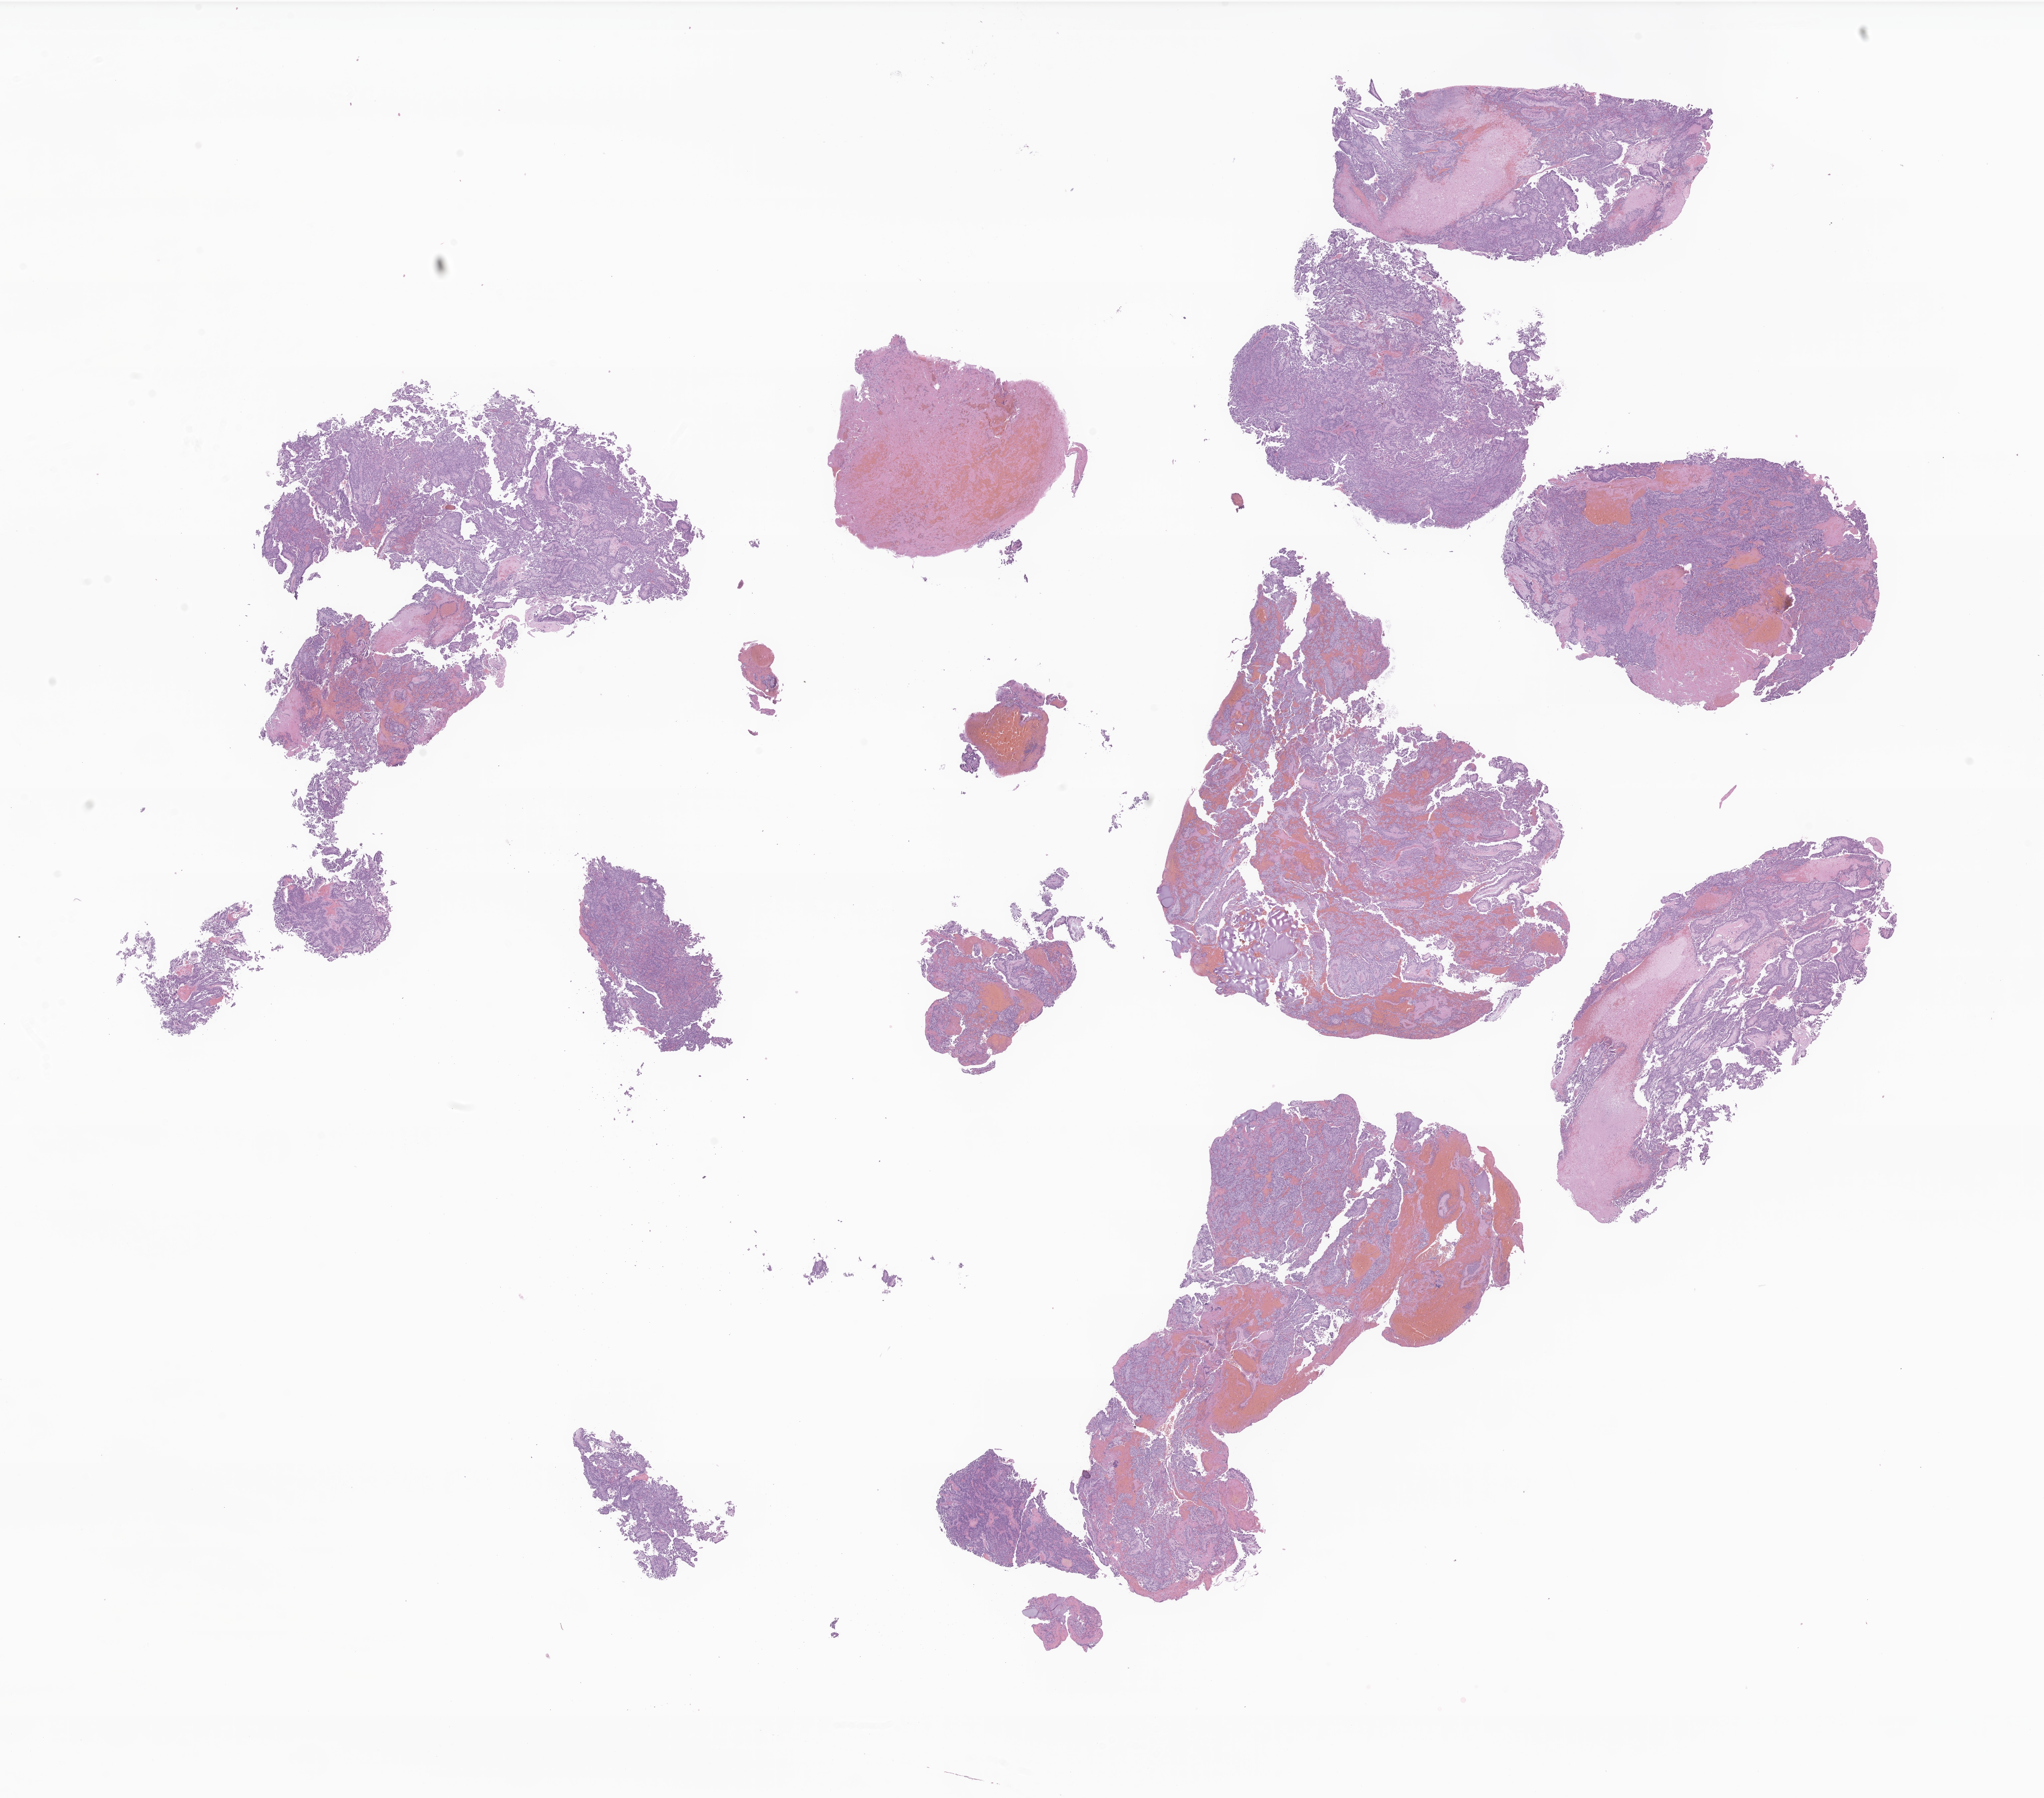
H&E whole-slide image of tumor tissue from the brain, a low-resolution overview of the entire scanned area, about 25.9 x 22.8 mm; formalin-fixed, paraffin-embedded (FFPE) tissue. Patient male; age 142 months (11 years 10 months).
- diagnosis (ICD-O-3 morphology term): Ependymoma, NOS